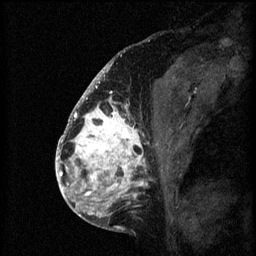
Breast MRI (dynamic contrast-enhanced), one sagittal slice. Position 29 of 60 along the scan axis. 3 images stored at this slice position (order not interpretable as contrast timing). 1.5 T. TE 4.2 ms, TR 8.2 ms. 2 mm slice thickness. 256 × 256 image matrix, field of view 180 × 180 mm. Patient: female, 41 years.
Outlined on this slice (semi-automatic segmentation, software-assisted and operator-edited):
- analysis volume of interest (the breast-tissue region the enhancement analysis was run in; not a lesion): bounding box (x1, y1, x2, y2) in pixels: (72, 108, 172, 205)
- tumour enhancement mask (voxels above the 70 % enhancement threshold inside the analysis volume of interest): (72, 108, 149, 205)